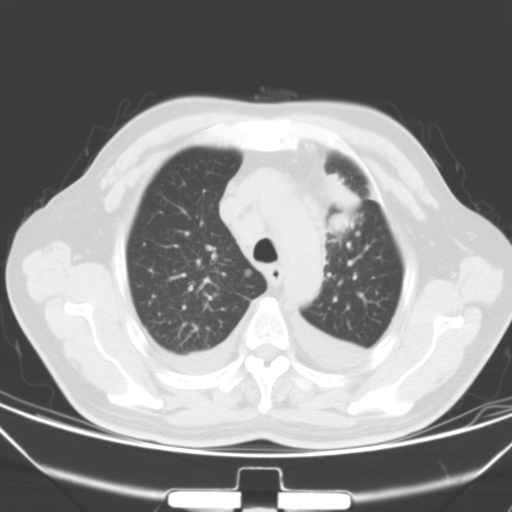
Chest CT, one axial slice; position 49 of 66 along the scan axis; 120 kVp; lung window (W 1500 / L -600 HU); 512 × 512 image matrix, field of view 352 × 352 mm. Patient: male, 66 years. From the clinical record (not read from this slice): clinical TNM (as recorded): T1c N0 M0.
Annotated regions visible in this slice (rectangle marked by the reading radiologist):
- lung tumour (recorded histology: adenocarcinoma): bounding box <324,172,358,230> (left, top, right, bottom; pixels)